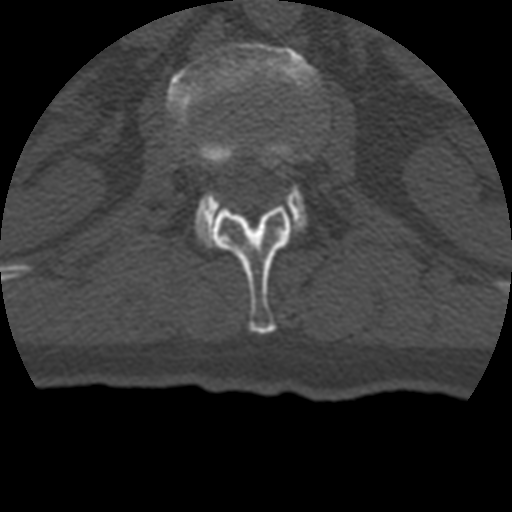
CT including the spine, one axial slice; position 134 of 399 along the scan axis; reconstruction kernel STANDARD; 120 kVp; bone window (W 1800 / L 400 HU); 1.25 mm slice thickness; 512 × 512 image matrix, field of view 160 × 160 mm. Patient age 69 years. Case-level facts recorded for this patient, not image findings: primary cancer: prostate.
Annotated regions visible in this slice (semi-automatic segmentation, software-assisted and operator-edited):
- L1 vertebra: box from (x=212, y=148) to (x=292, y=334) px
- L2 vertebra: (x=167, y=43)–(x=319, y=245)